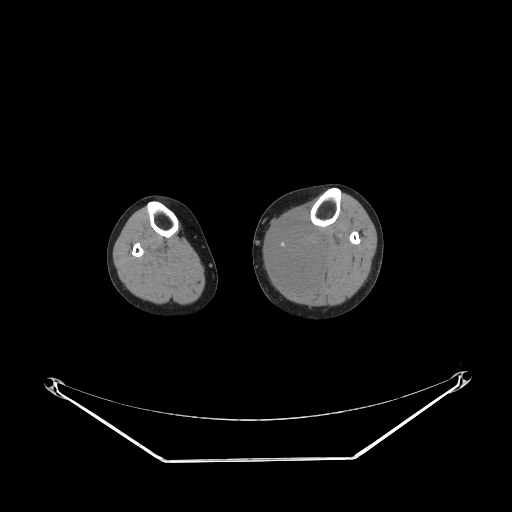
CT of an extremity soft-tissue mass (from a PET/CT study), one axial slice. Position 144 of 223 along the scan axis. Reconstruction kernel STANDARD. Soft-tissue window (W 400 / L 40 HU). 3.75 mm slice thickness. 512 × 512 image matrix, field of view 500 × 500 mm. Female patient. Case-level facts recorded for this patient, not image findings: histological type: extraskeletal high grade osteogenic sarcoma; grade: high; site of the primary tumour: left calf.
Outlined on this slice (expert contour drawn on MRI and transferred to this co-registered scan by the dataset authors):
- gross tumour volume (mass): box from (x=270, y=221) to (x=325, y=287) px